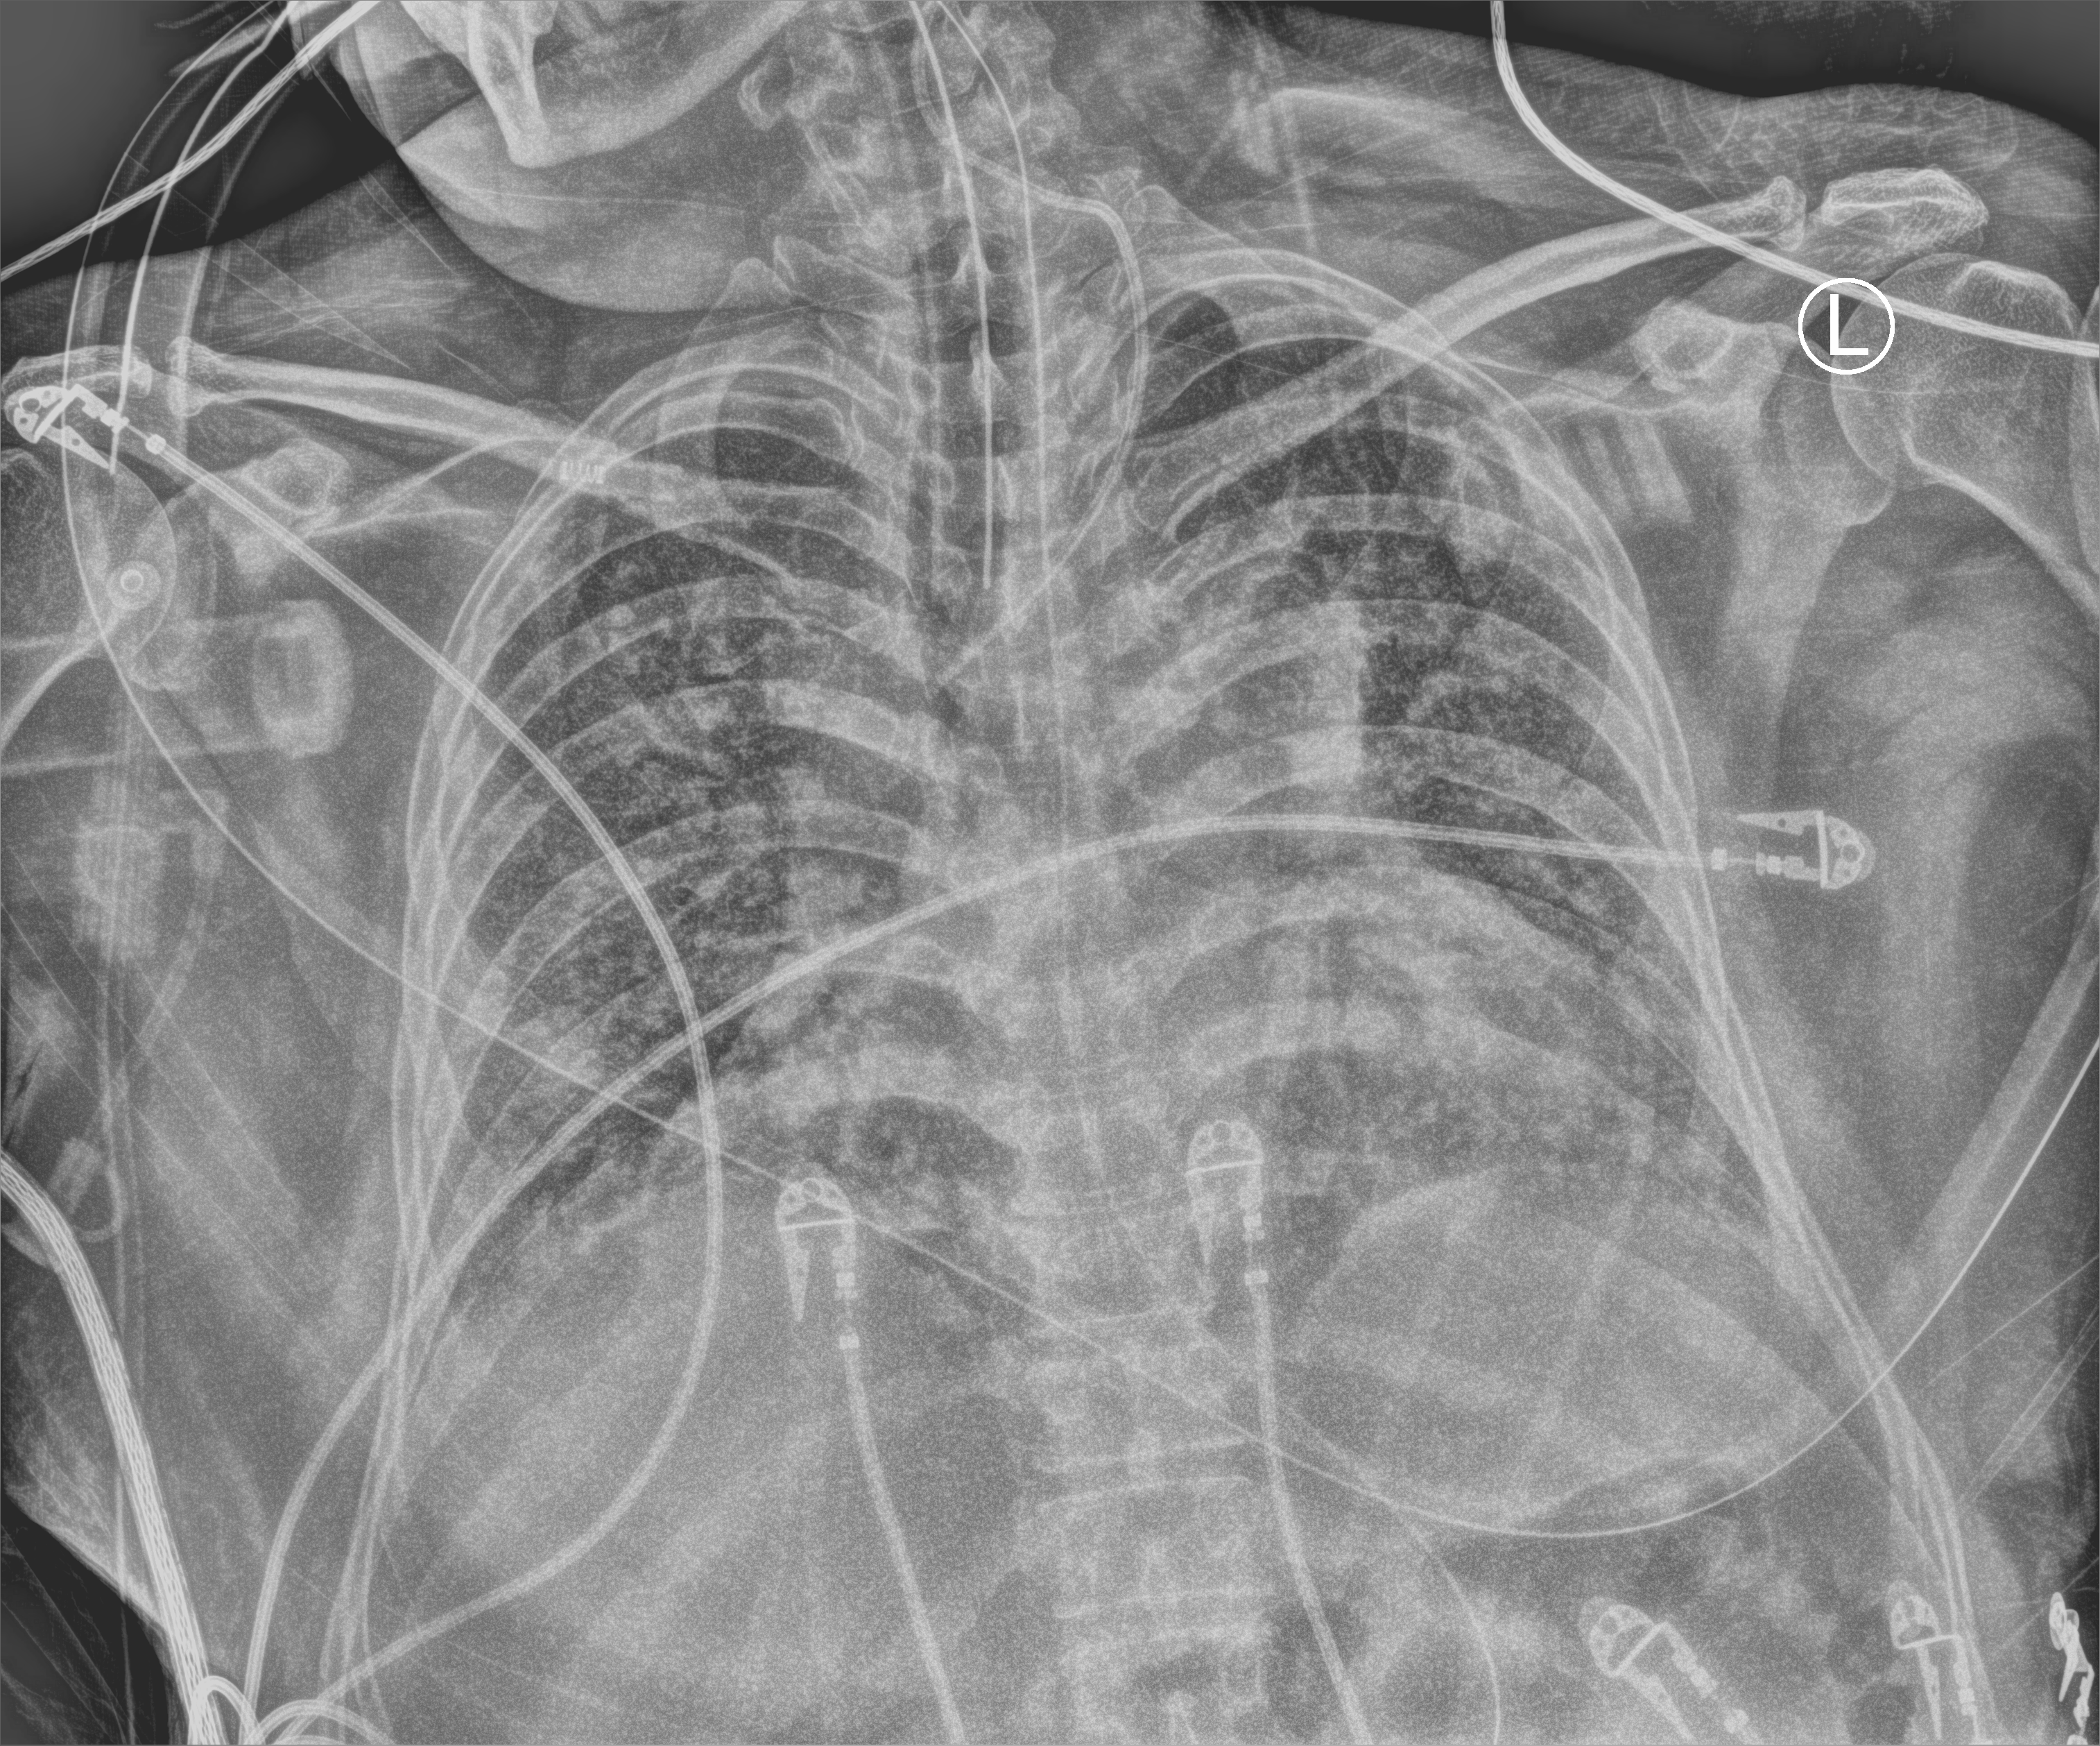
Bedside chest radiograph (computed radiography); anteroposterior (AP) projection. Adult patient hospitalised with COVID-19, age 18–59 years.
Admission-level facts for this patient (not findings on this image; timing relative to this image not recorded):
- mechanically ventilated during this hospital stay: yes